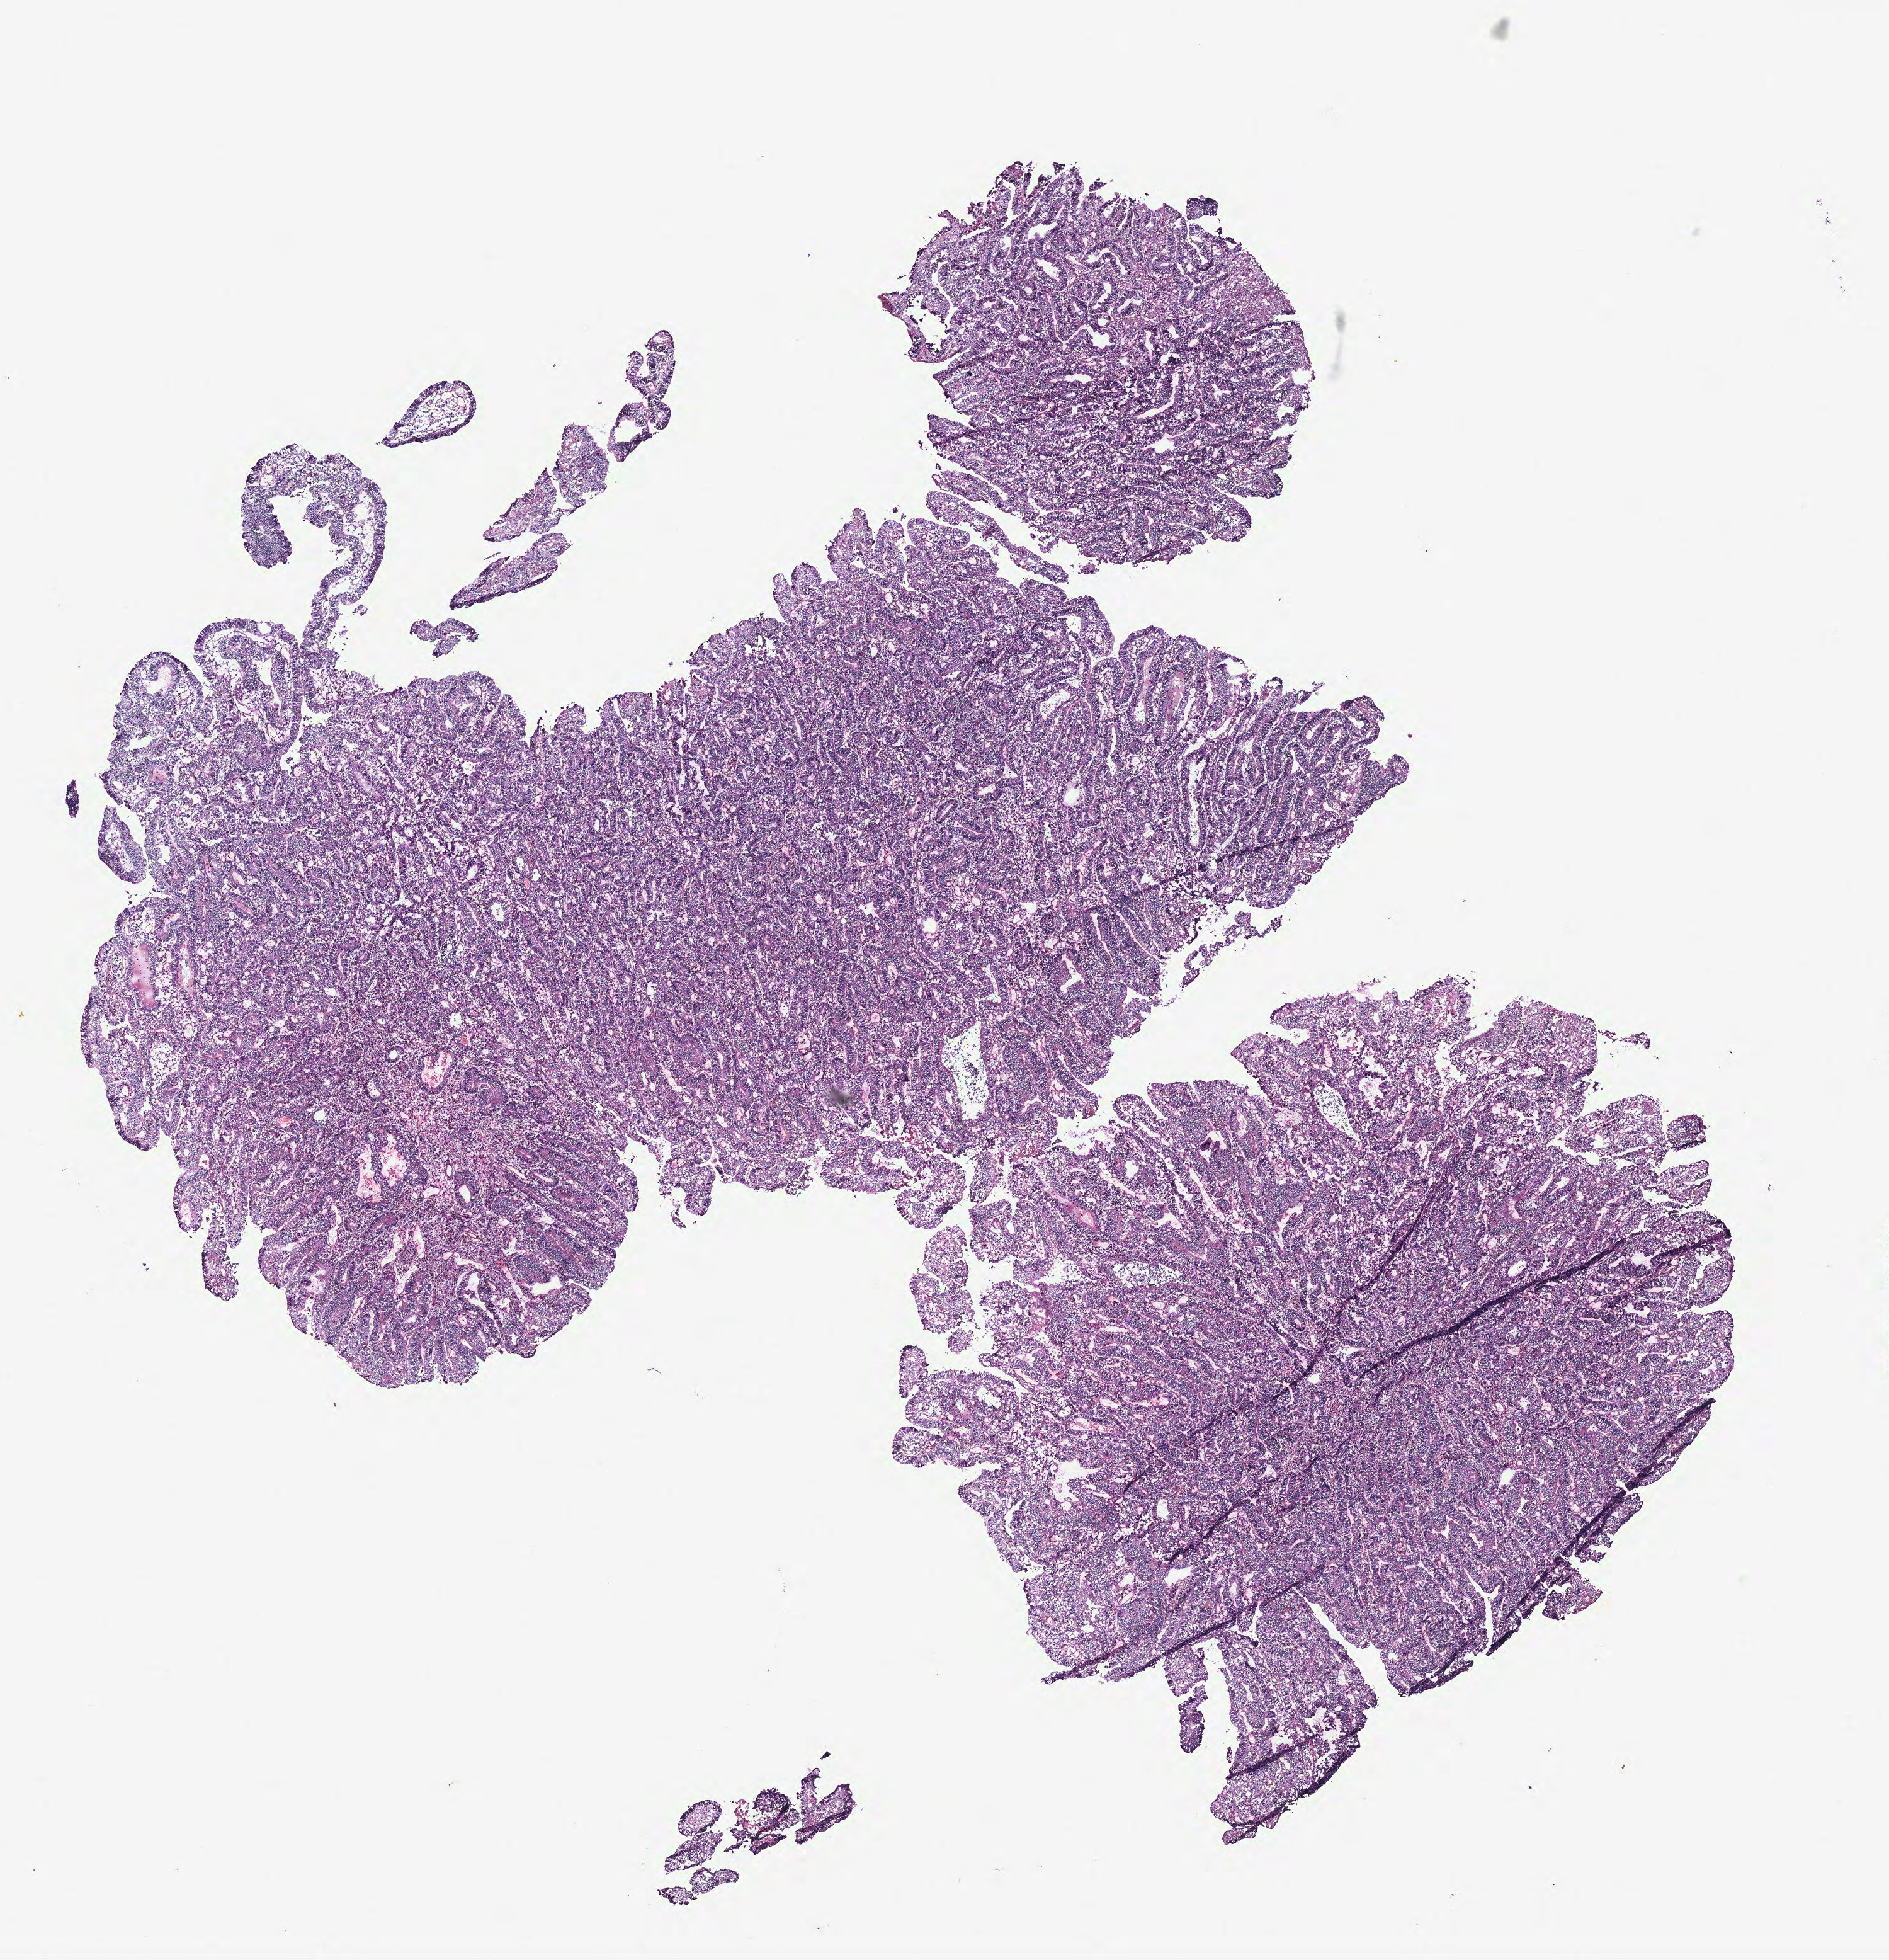
Digitized Hematoxylin and eosin (H&E) stained tissue section (whole slide) — shown as a low-resolution overview of the whole scanned area (about 12.0 x 12.5 mm), colon, tissue type not recorded.
Patient diagnosis (cohort enrolment): colon cancer (colon).